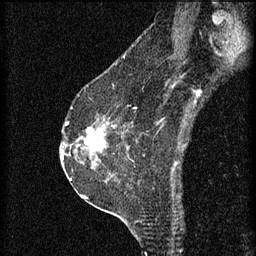
Breast MRI (dynamic contrast-enhanced), one sagittal slice. Position 40 of 60 along the scan axis. 3 images stored at this slice position (order not interpretable as contrast timing). 1.5 T. TE 4.2 ms, TR 8.2 ms. 2 mm slice thickness. 256 × 256 image matrix, field of view 180 × 180 mm. Patient: female, 60 years.
Outlined on this slice (semi-automatic segmentation, software-assisted and operator-edited):
- analysis volume of interest (the breast-tissue region the enhancement analysis was run in; not a lesion): box from (x=74, y=124) to (x=111, y=159) px
- tumour enhancement mask (voxels above the 70 % enhancement threshold inside the analysis volume of interest): (x=86, y=128)–(x=105, y=153)